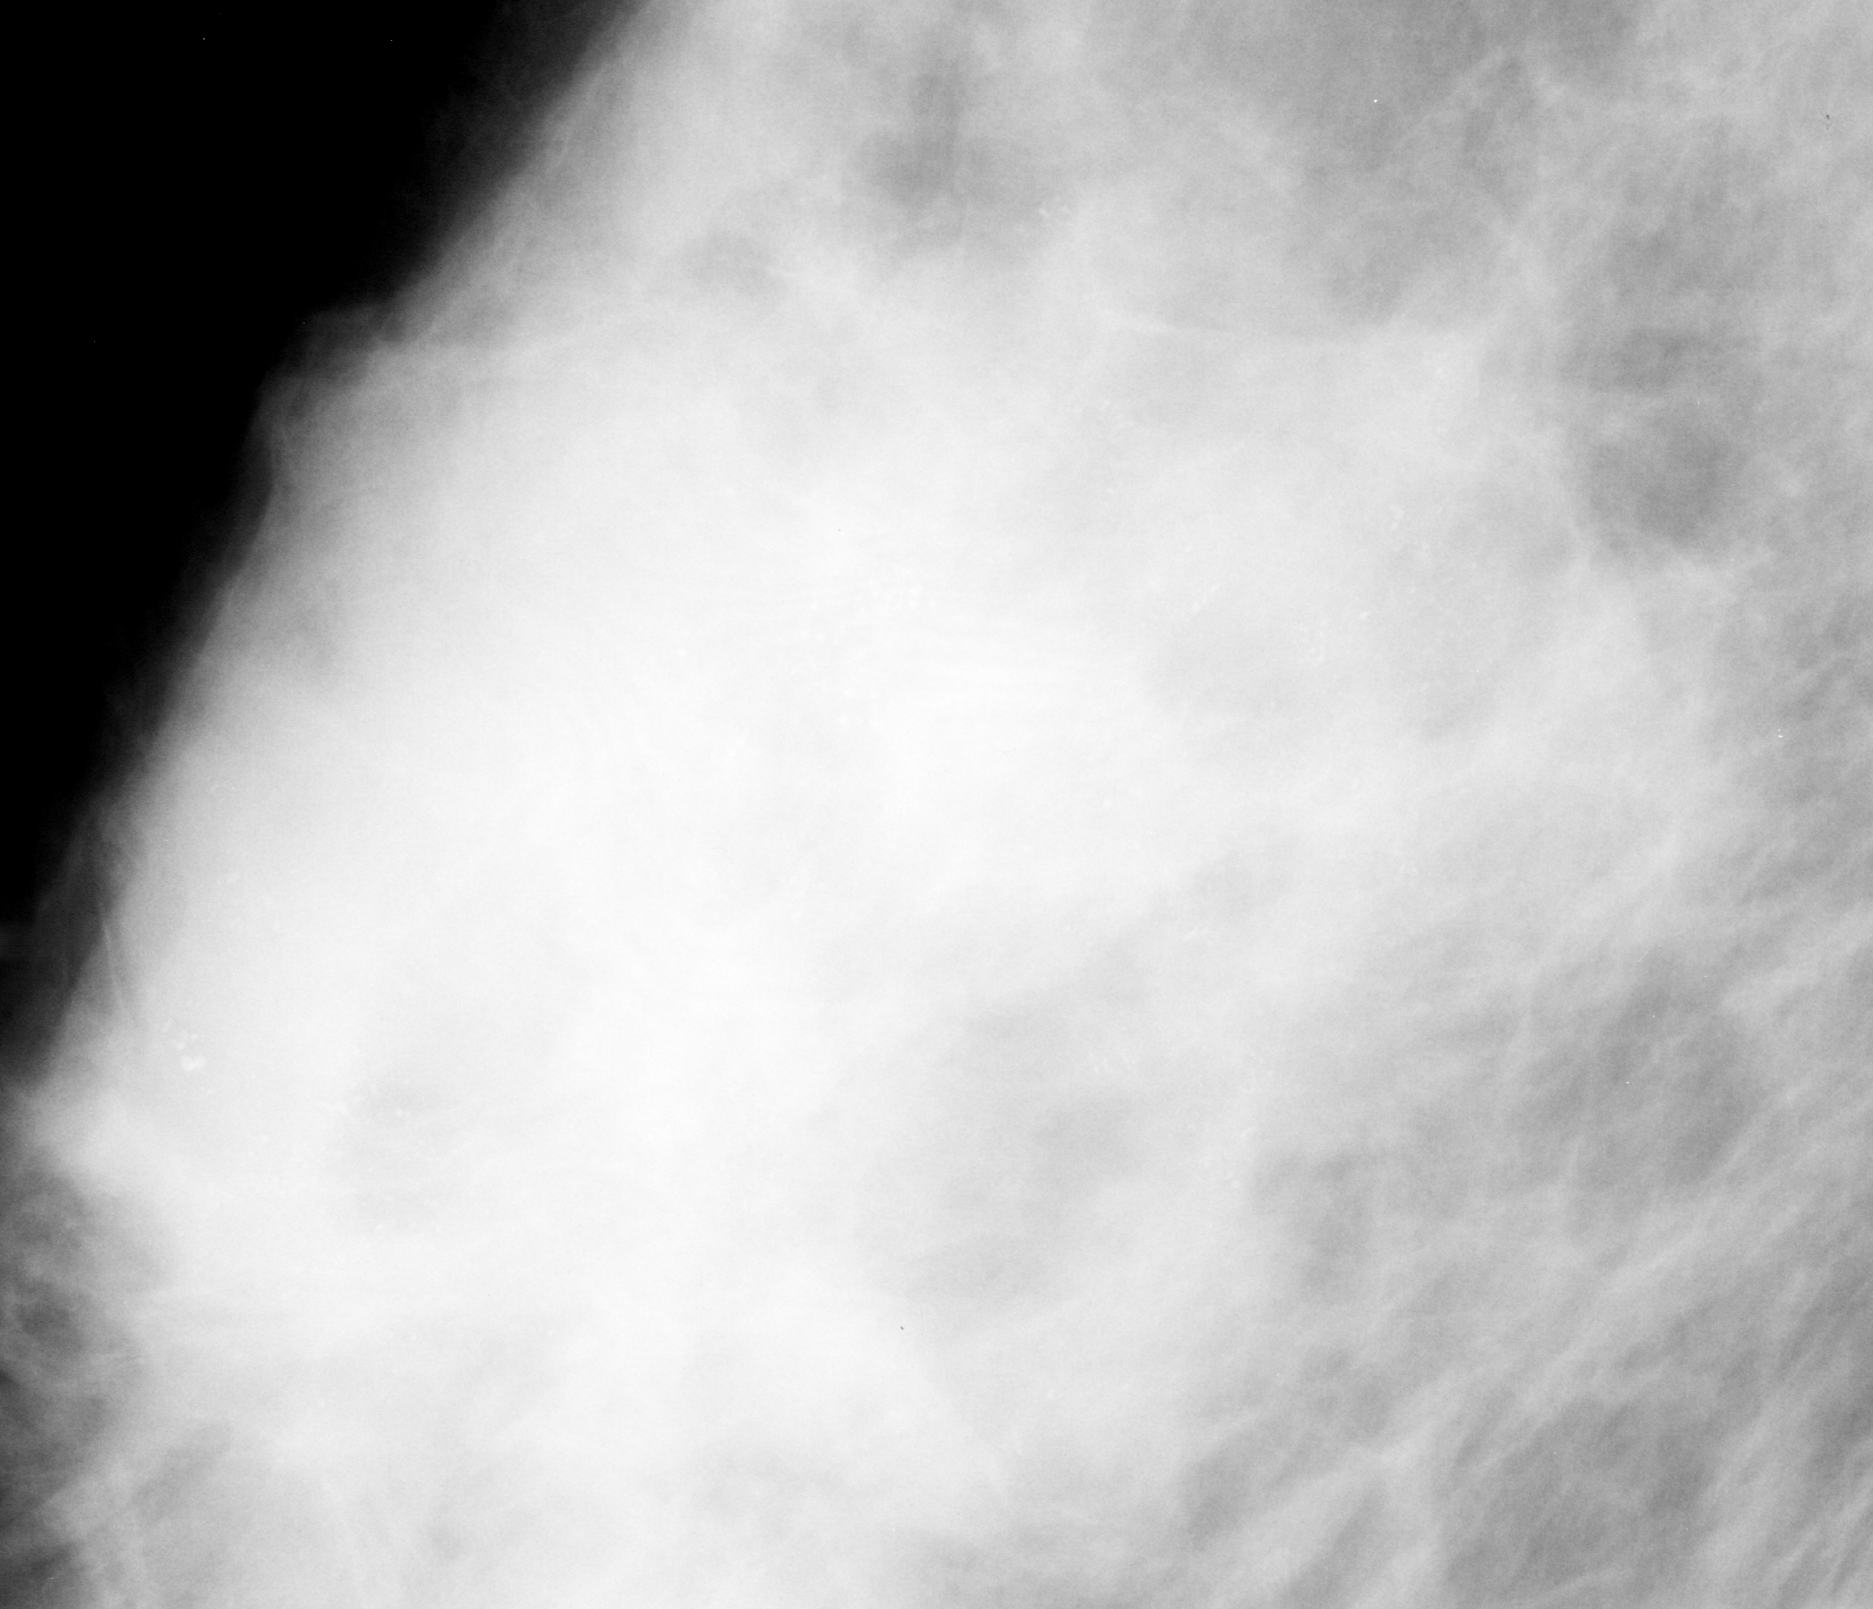
Region of interest cut from a scanned film mammogram (one marked finding), right breast, MLO view, BI-RADS breast density category 3 (scale 1–4).
- Marked abnormality: calcifications, morphology pleomorphic, distribution regional; BI-RADS assessment category 5; subtlety rating 3 on a 1 (subtle) to 5 (obvious) scale; pathology result (as recorded, not read from the image): malignant.